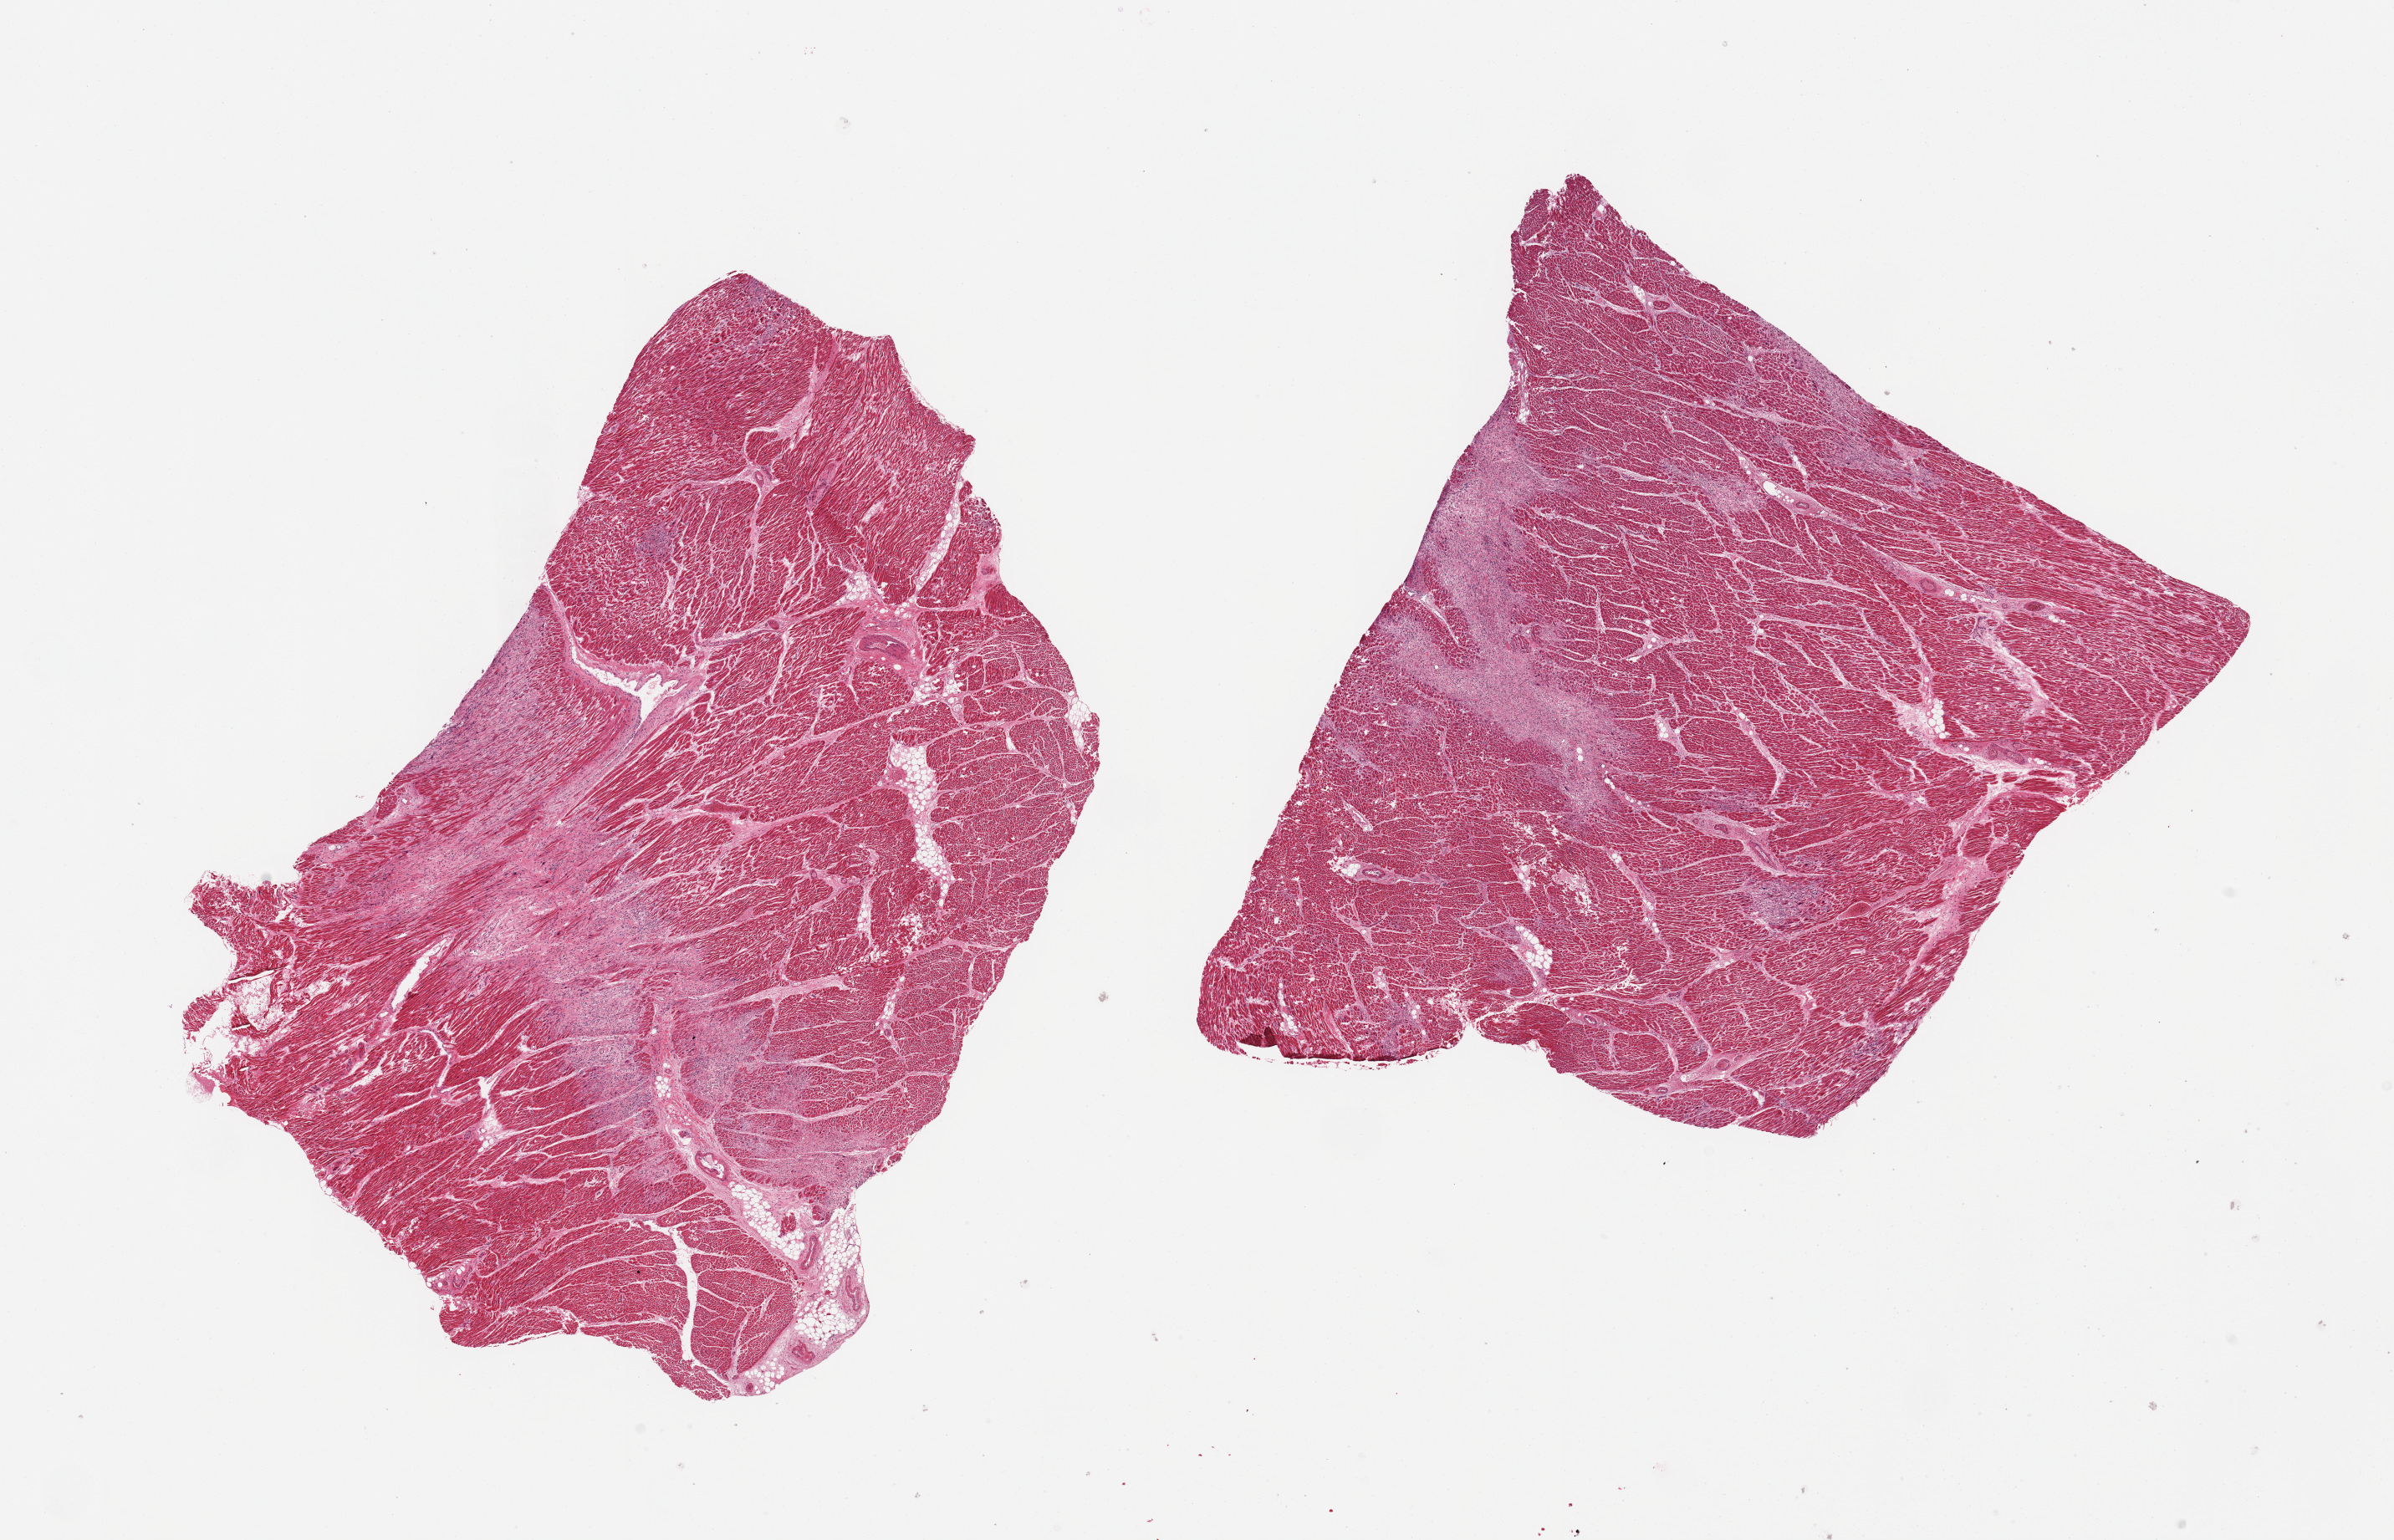
Whole-slide image, H&E stain, low-resolution overview of the scanned area, about 22.6 x 14.6 mm; PAXgene-fixed paraffin-embedded (PFPE) section; sampled site (target tissue): heart; donor tissue sample. Female donor.
Reviewer comment on this tissue sample: 2 pieces; extensive interstitial myocarditis (10 & 30% of the surface area) not typical of infarction, possibly viral or autoimmune myocarditis.